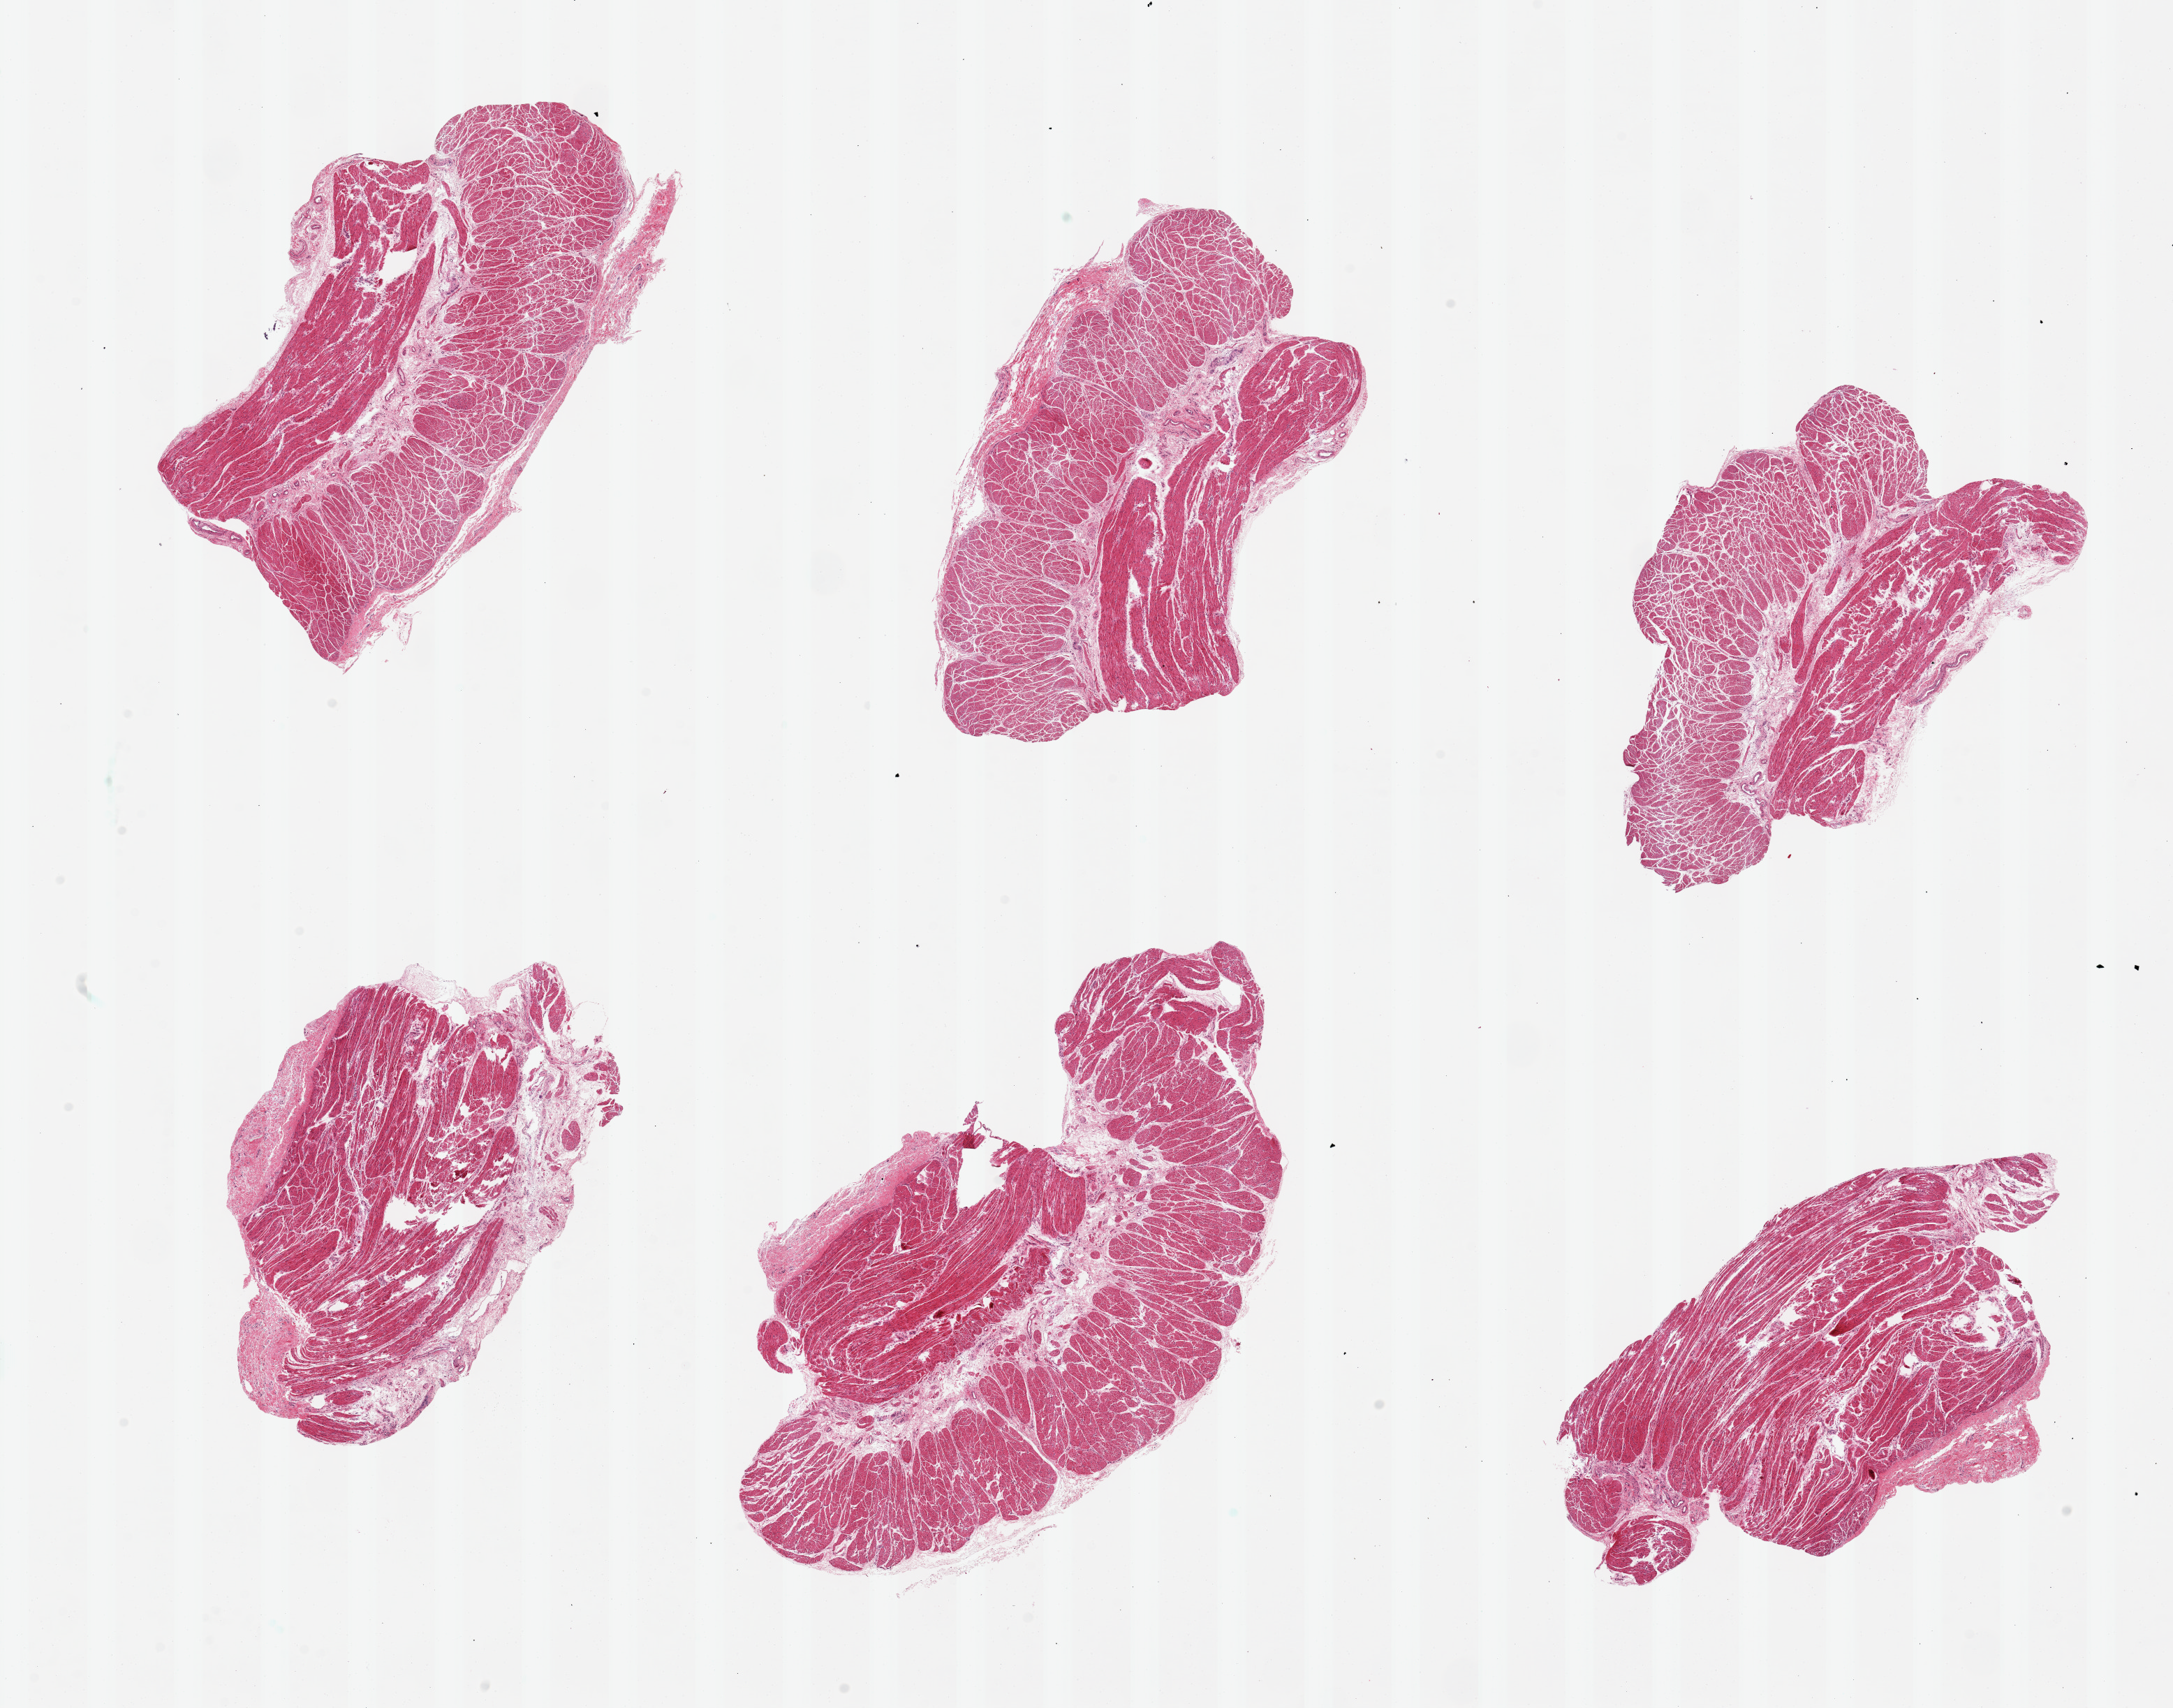
Whole-slide image, H&E stain — shown as a low-resolution overview of the whole scanned area (about 24.6 x 19.3 mm); PAXgene-fixed paraffin-embedded (PFPE) section; target tissue: esophageal muscle; tissue donor sample. Donor sex: female.
Pathologist's review note for this sample: 6 pieces, up to 9x5mm; well trimmed musc. propria; good ganglion cells.